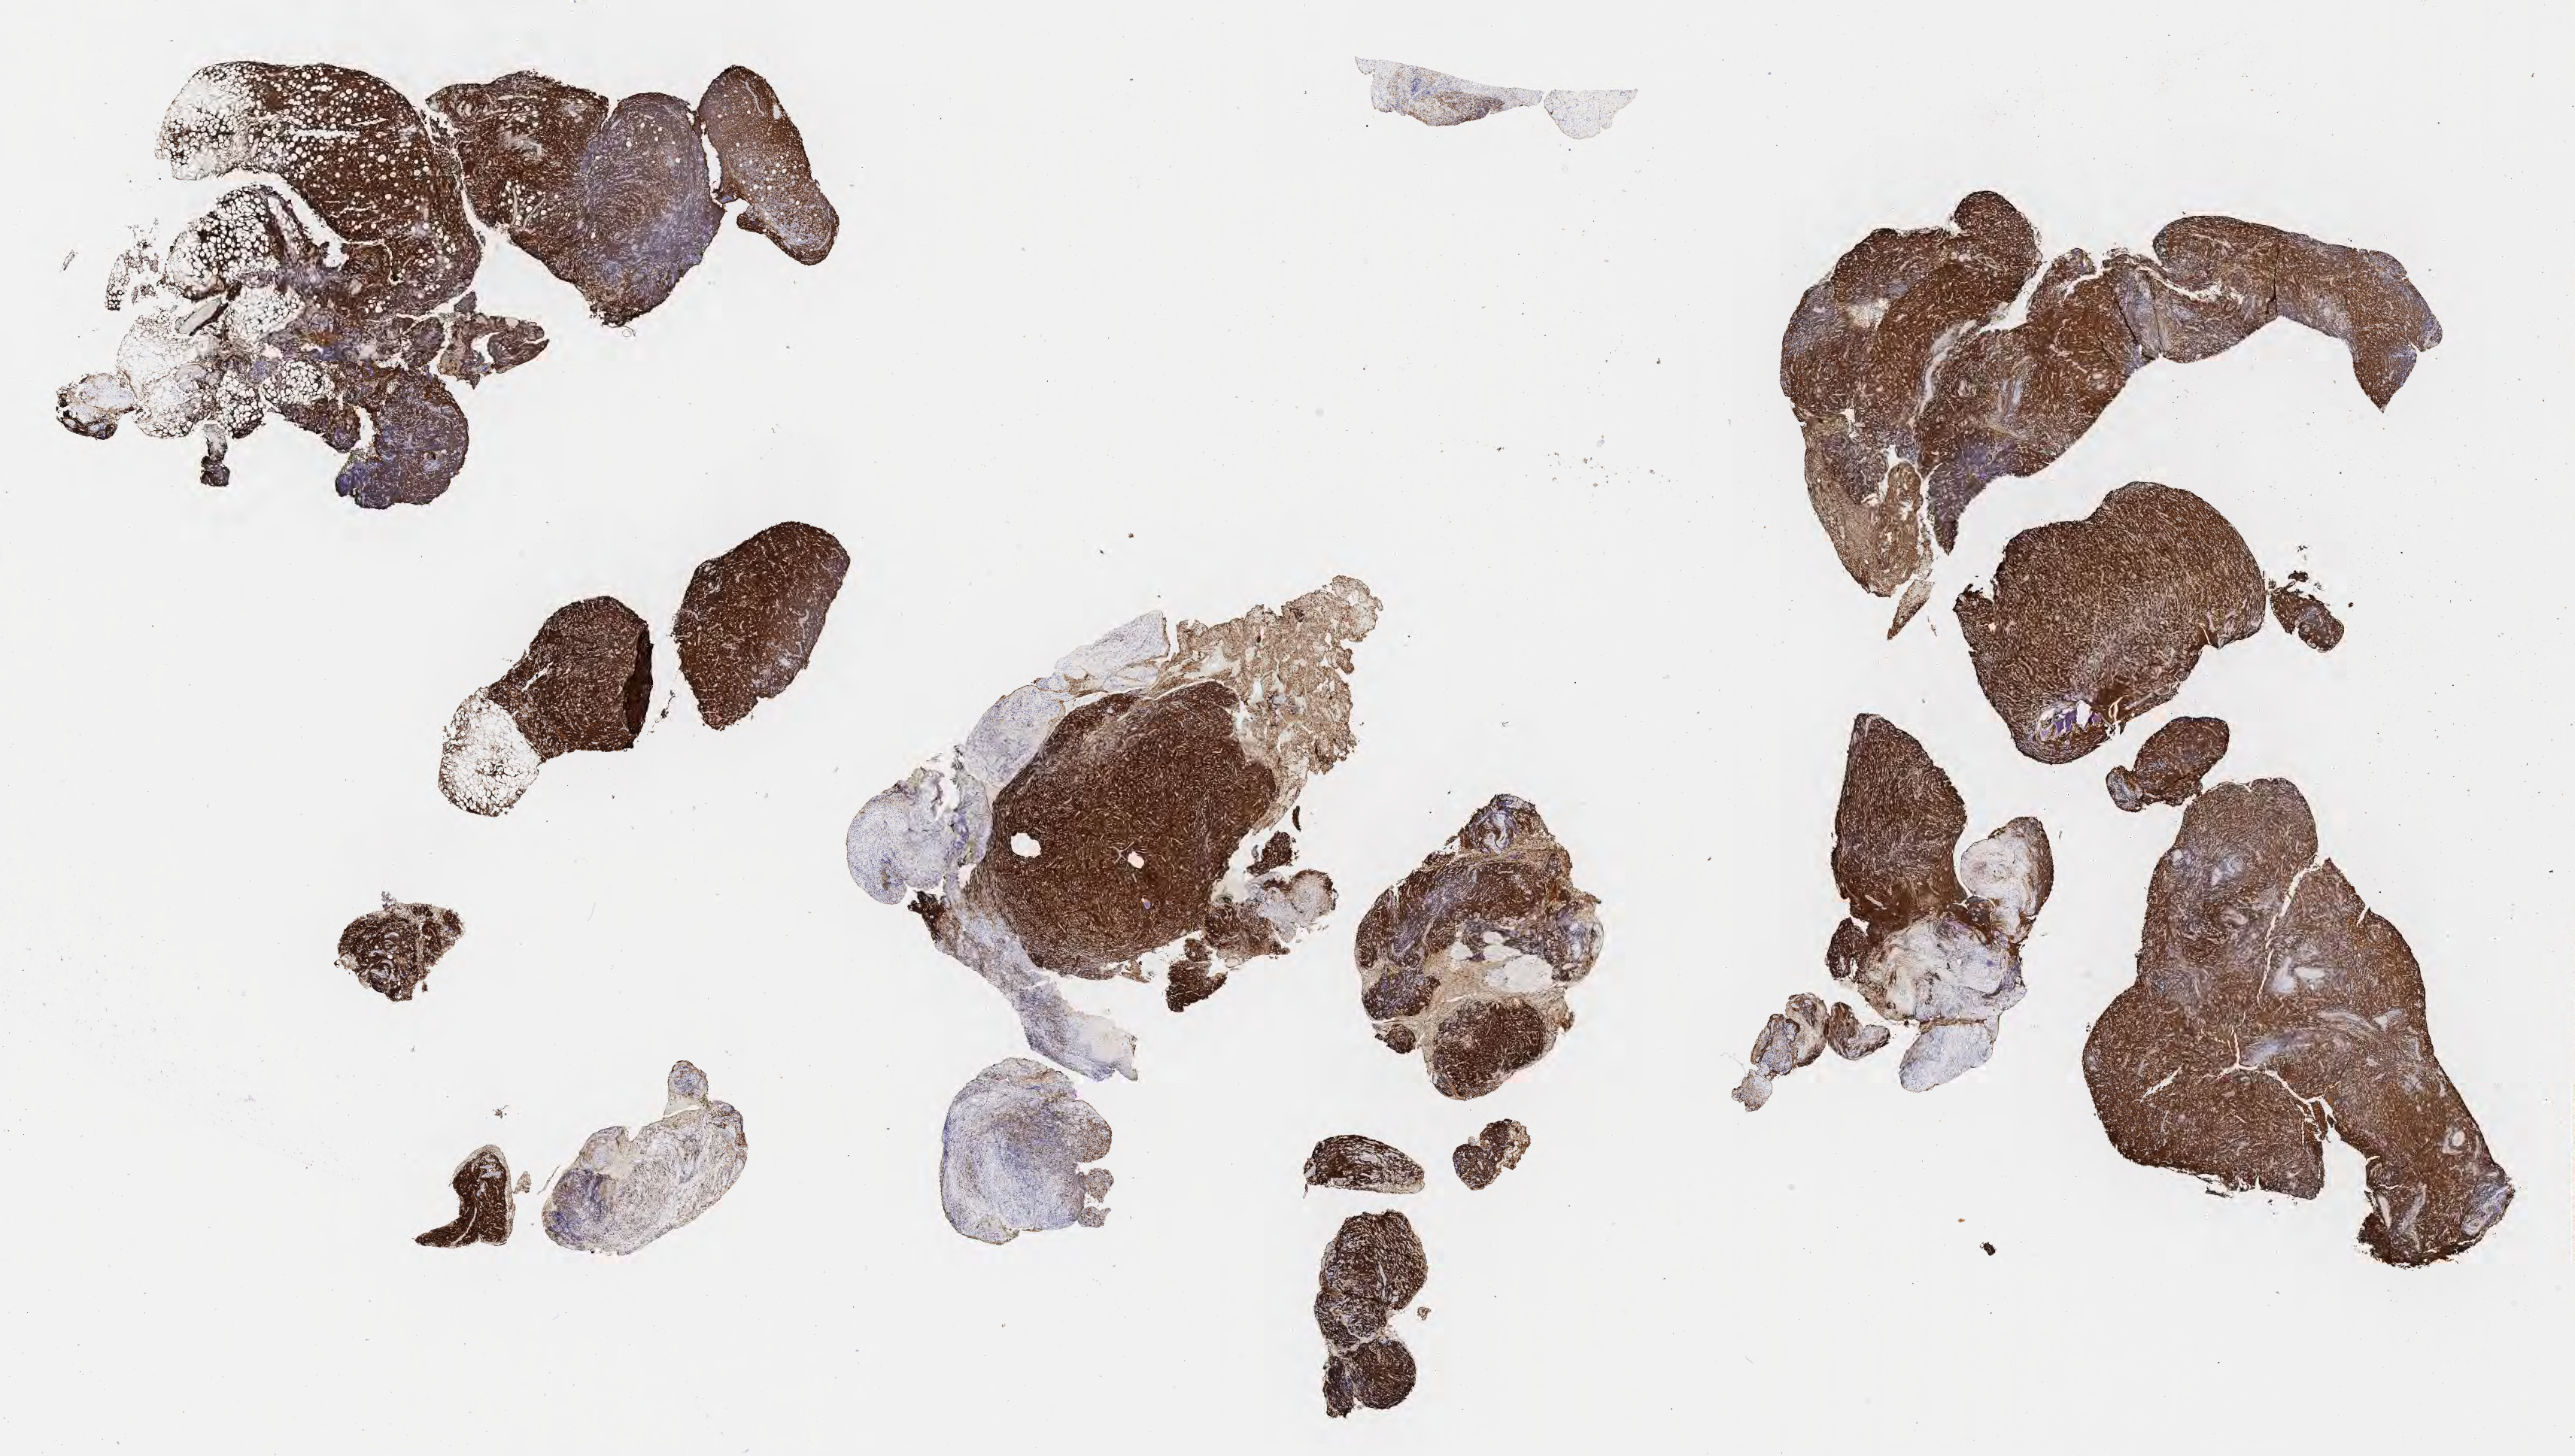
Immunohistochemistry (IHC) whole-slide image stained for CD79a — whole scanned area (about 27.7 x 15.7 mm) shown as a low-resolution overview. Tumor tissue. Patient male; aged 45.
Diagnosis: Diffuse large B-cell lymphoma, NOS.